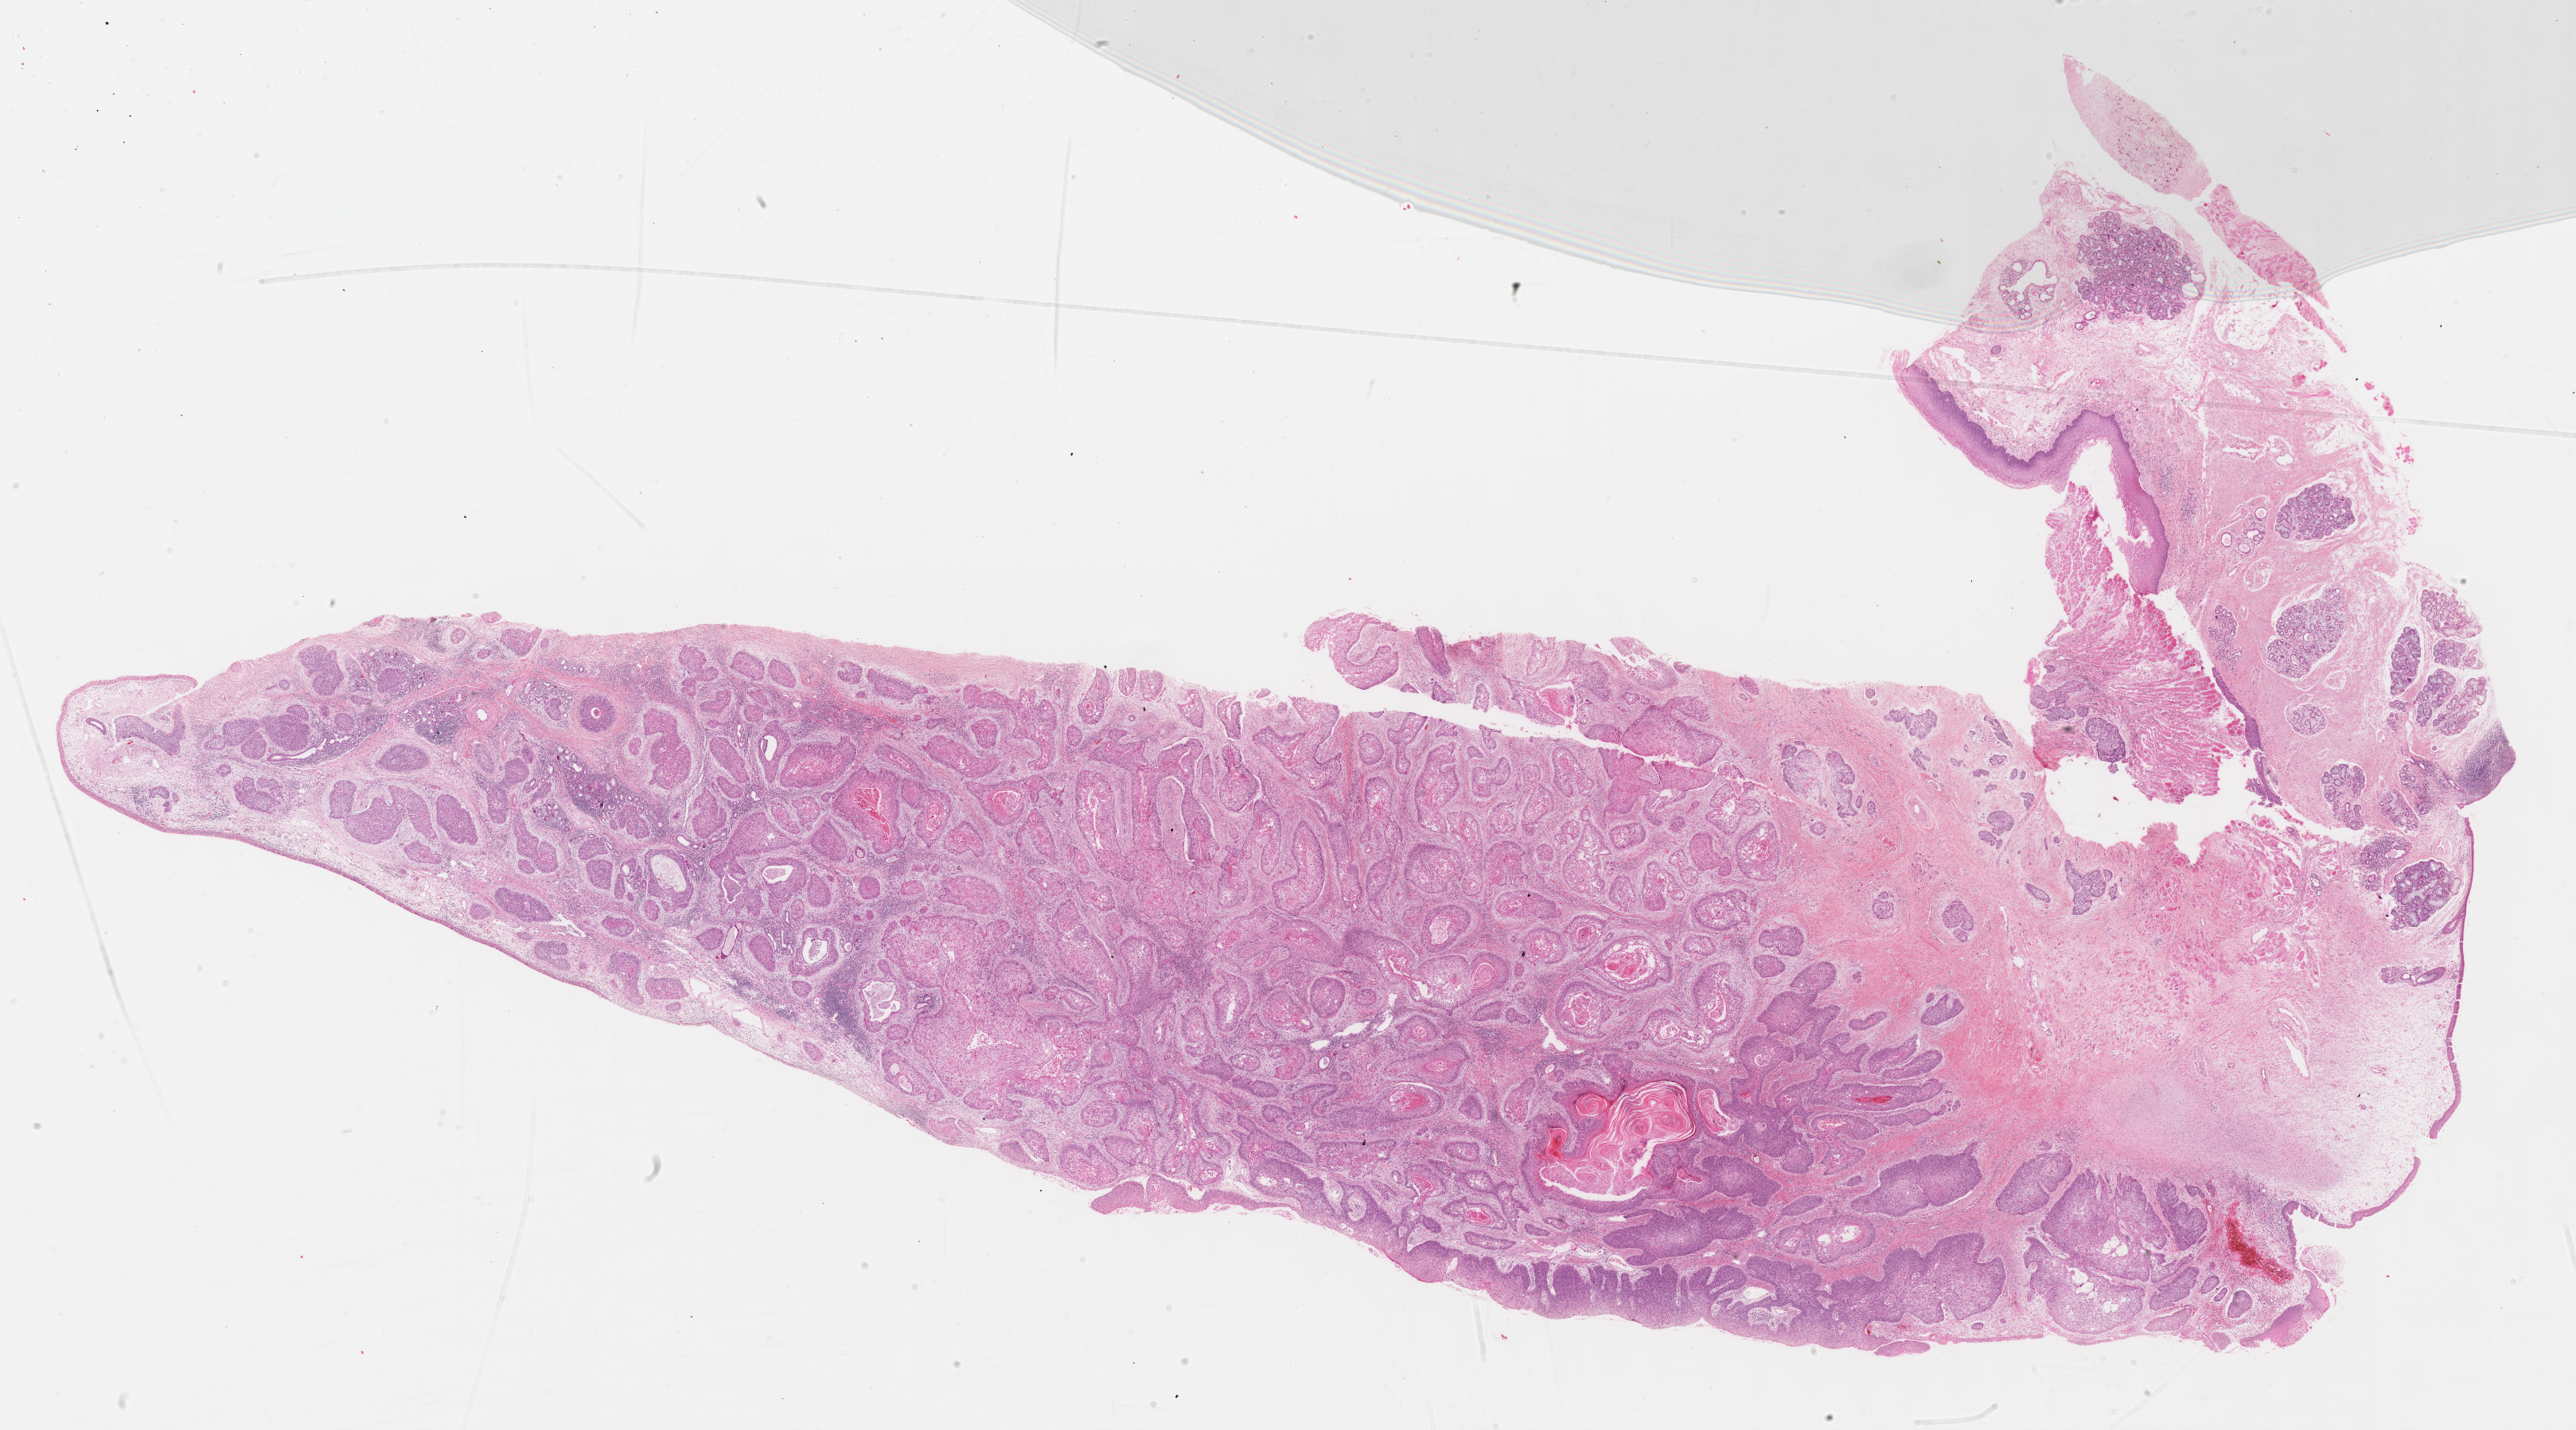
H&E-stained whole-slide image, a low-resolution overview of the entire scanned area, about 26.2 x 14.5 mm; formalin-fixed paraffin-embedded (FFPE) diagnostic section; sample: primary tumour, head and neck. Female patient; age at initial diagnosis 82 years. Histologic grade: G2 (moderately differentiated).
Diagnosis: Squamous cell carcinoma, NOS (larynx, NOS). AJCC pathologic stage: II (7th edition).